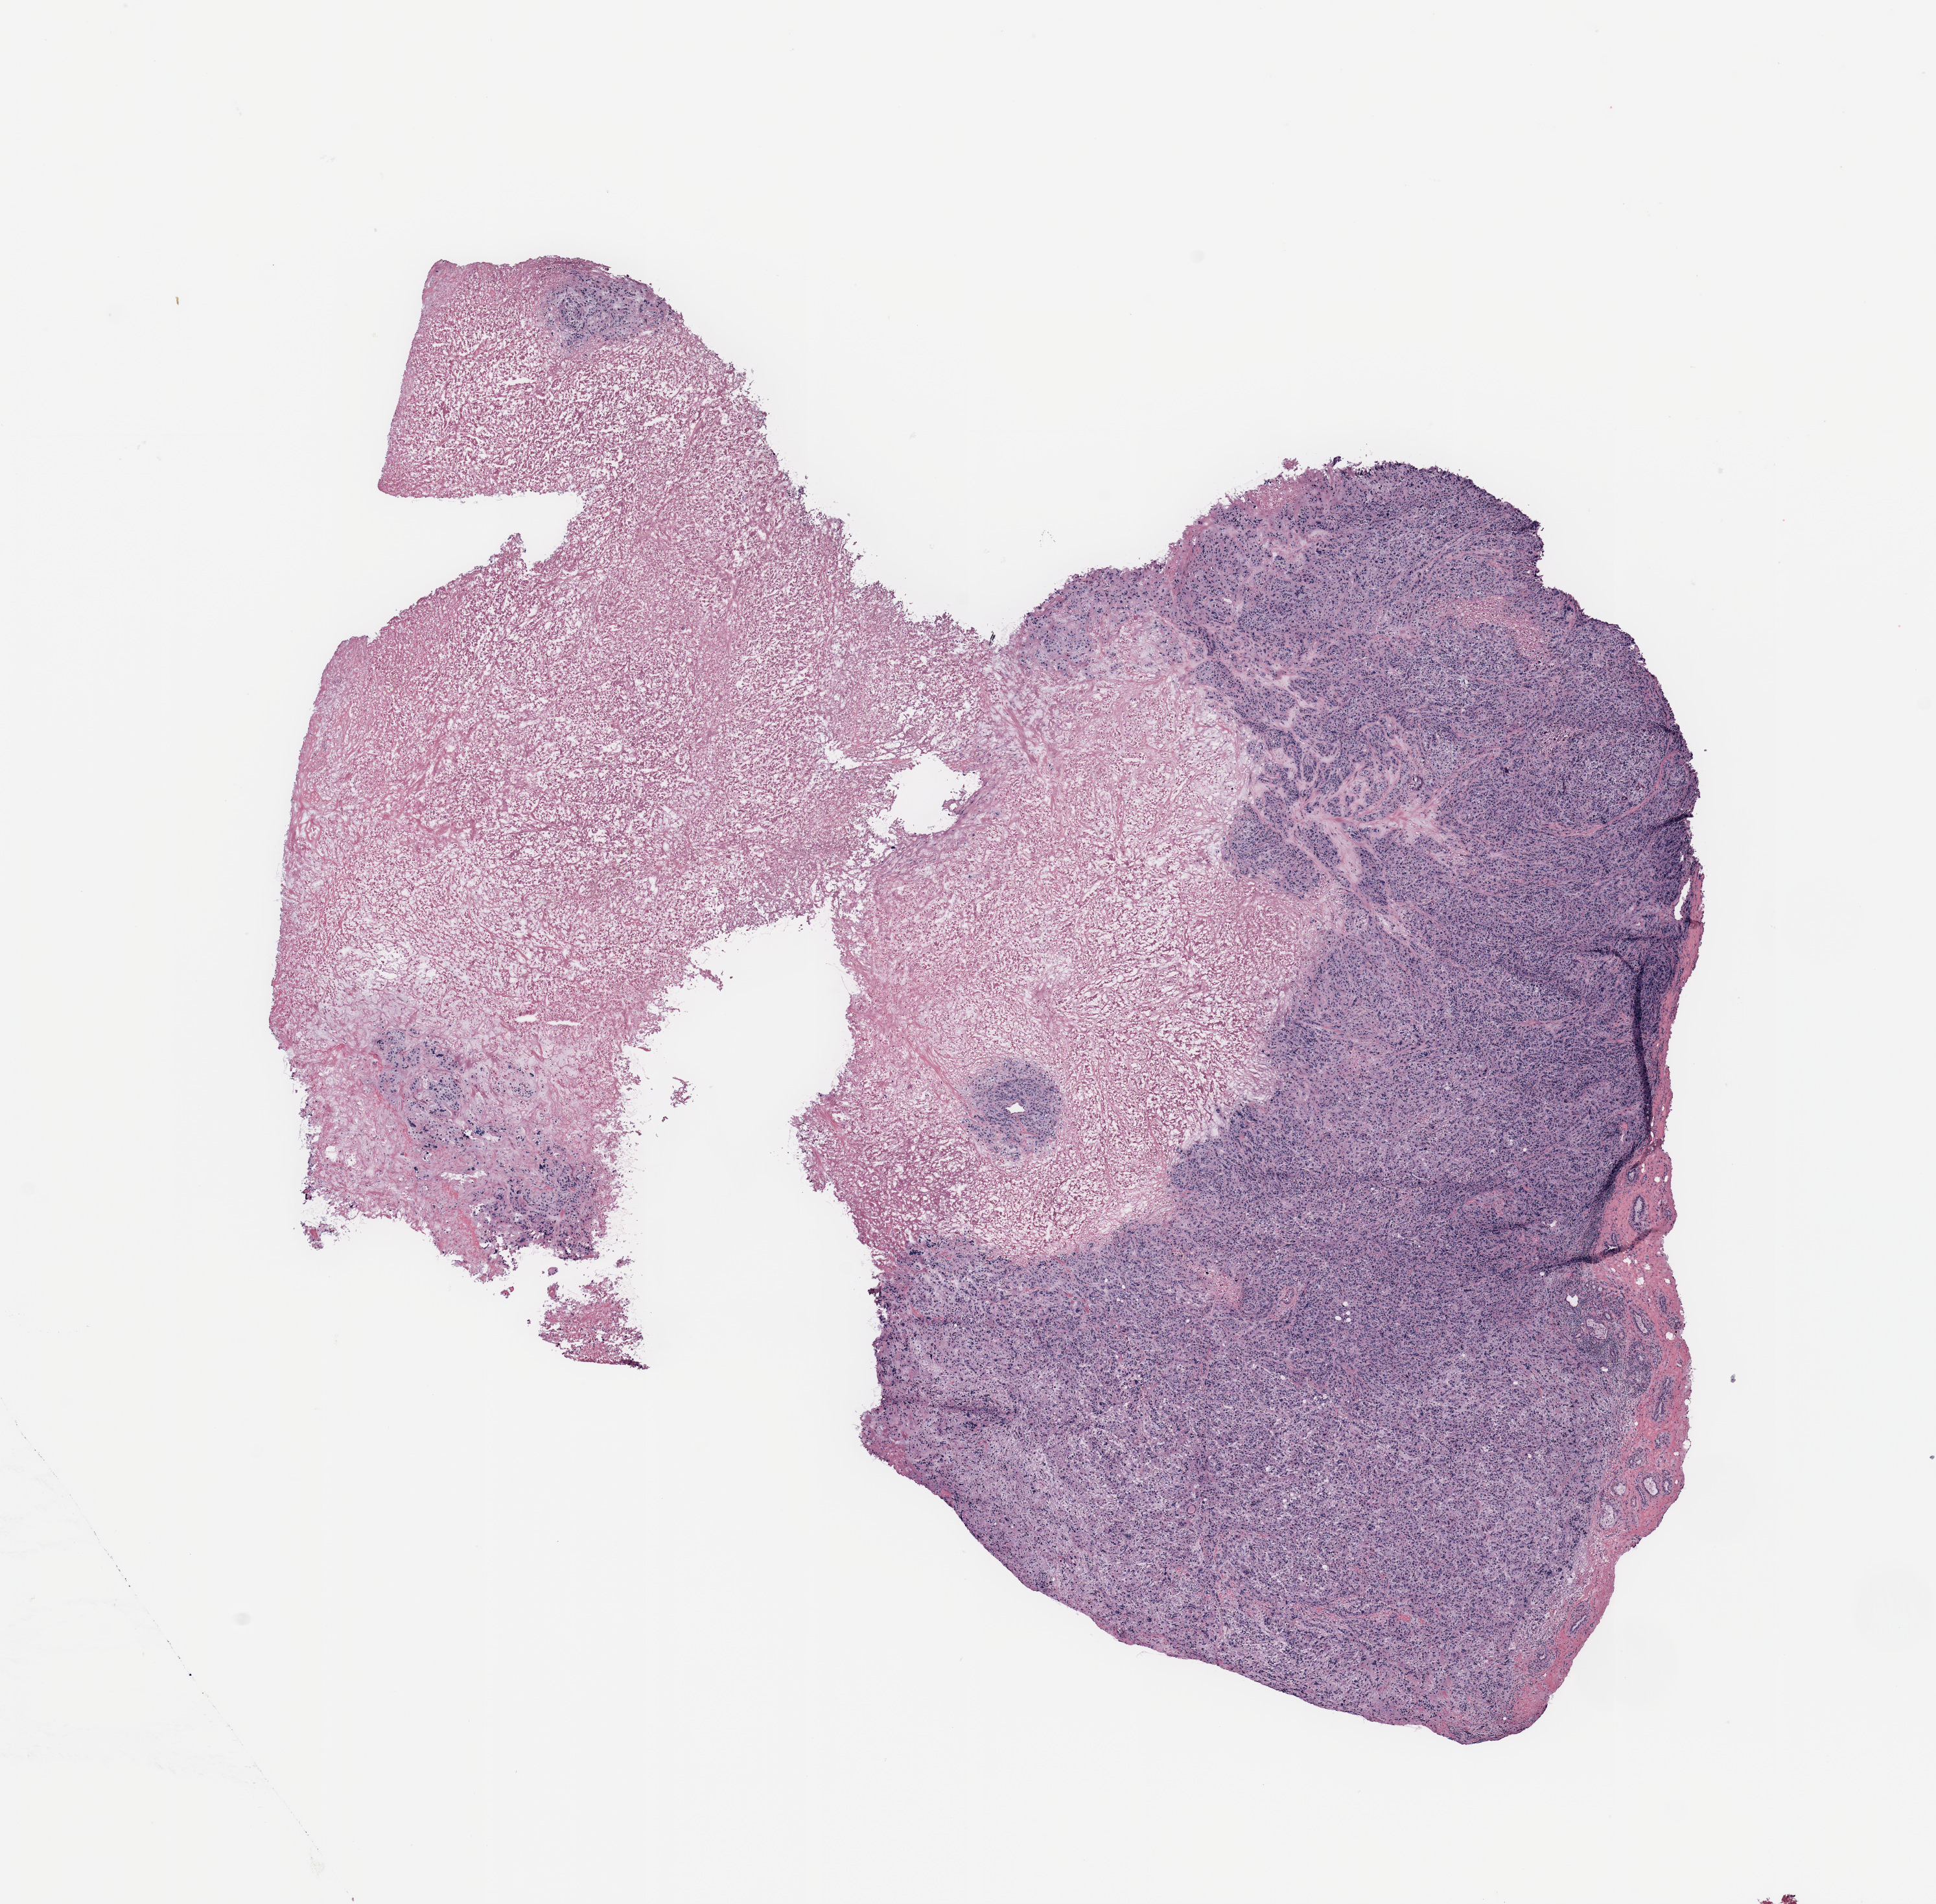
Whole-slide histology image, H&E-stained, whole scanned area (about 11.8 x 11.6 mm, from a 20x scan) shown as a low-resolution overview, tumour tissue sample, breast. 65-year-old female patient.
Histologic diagnosis: Infiltrating duct carcinoma, NOS.